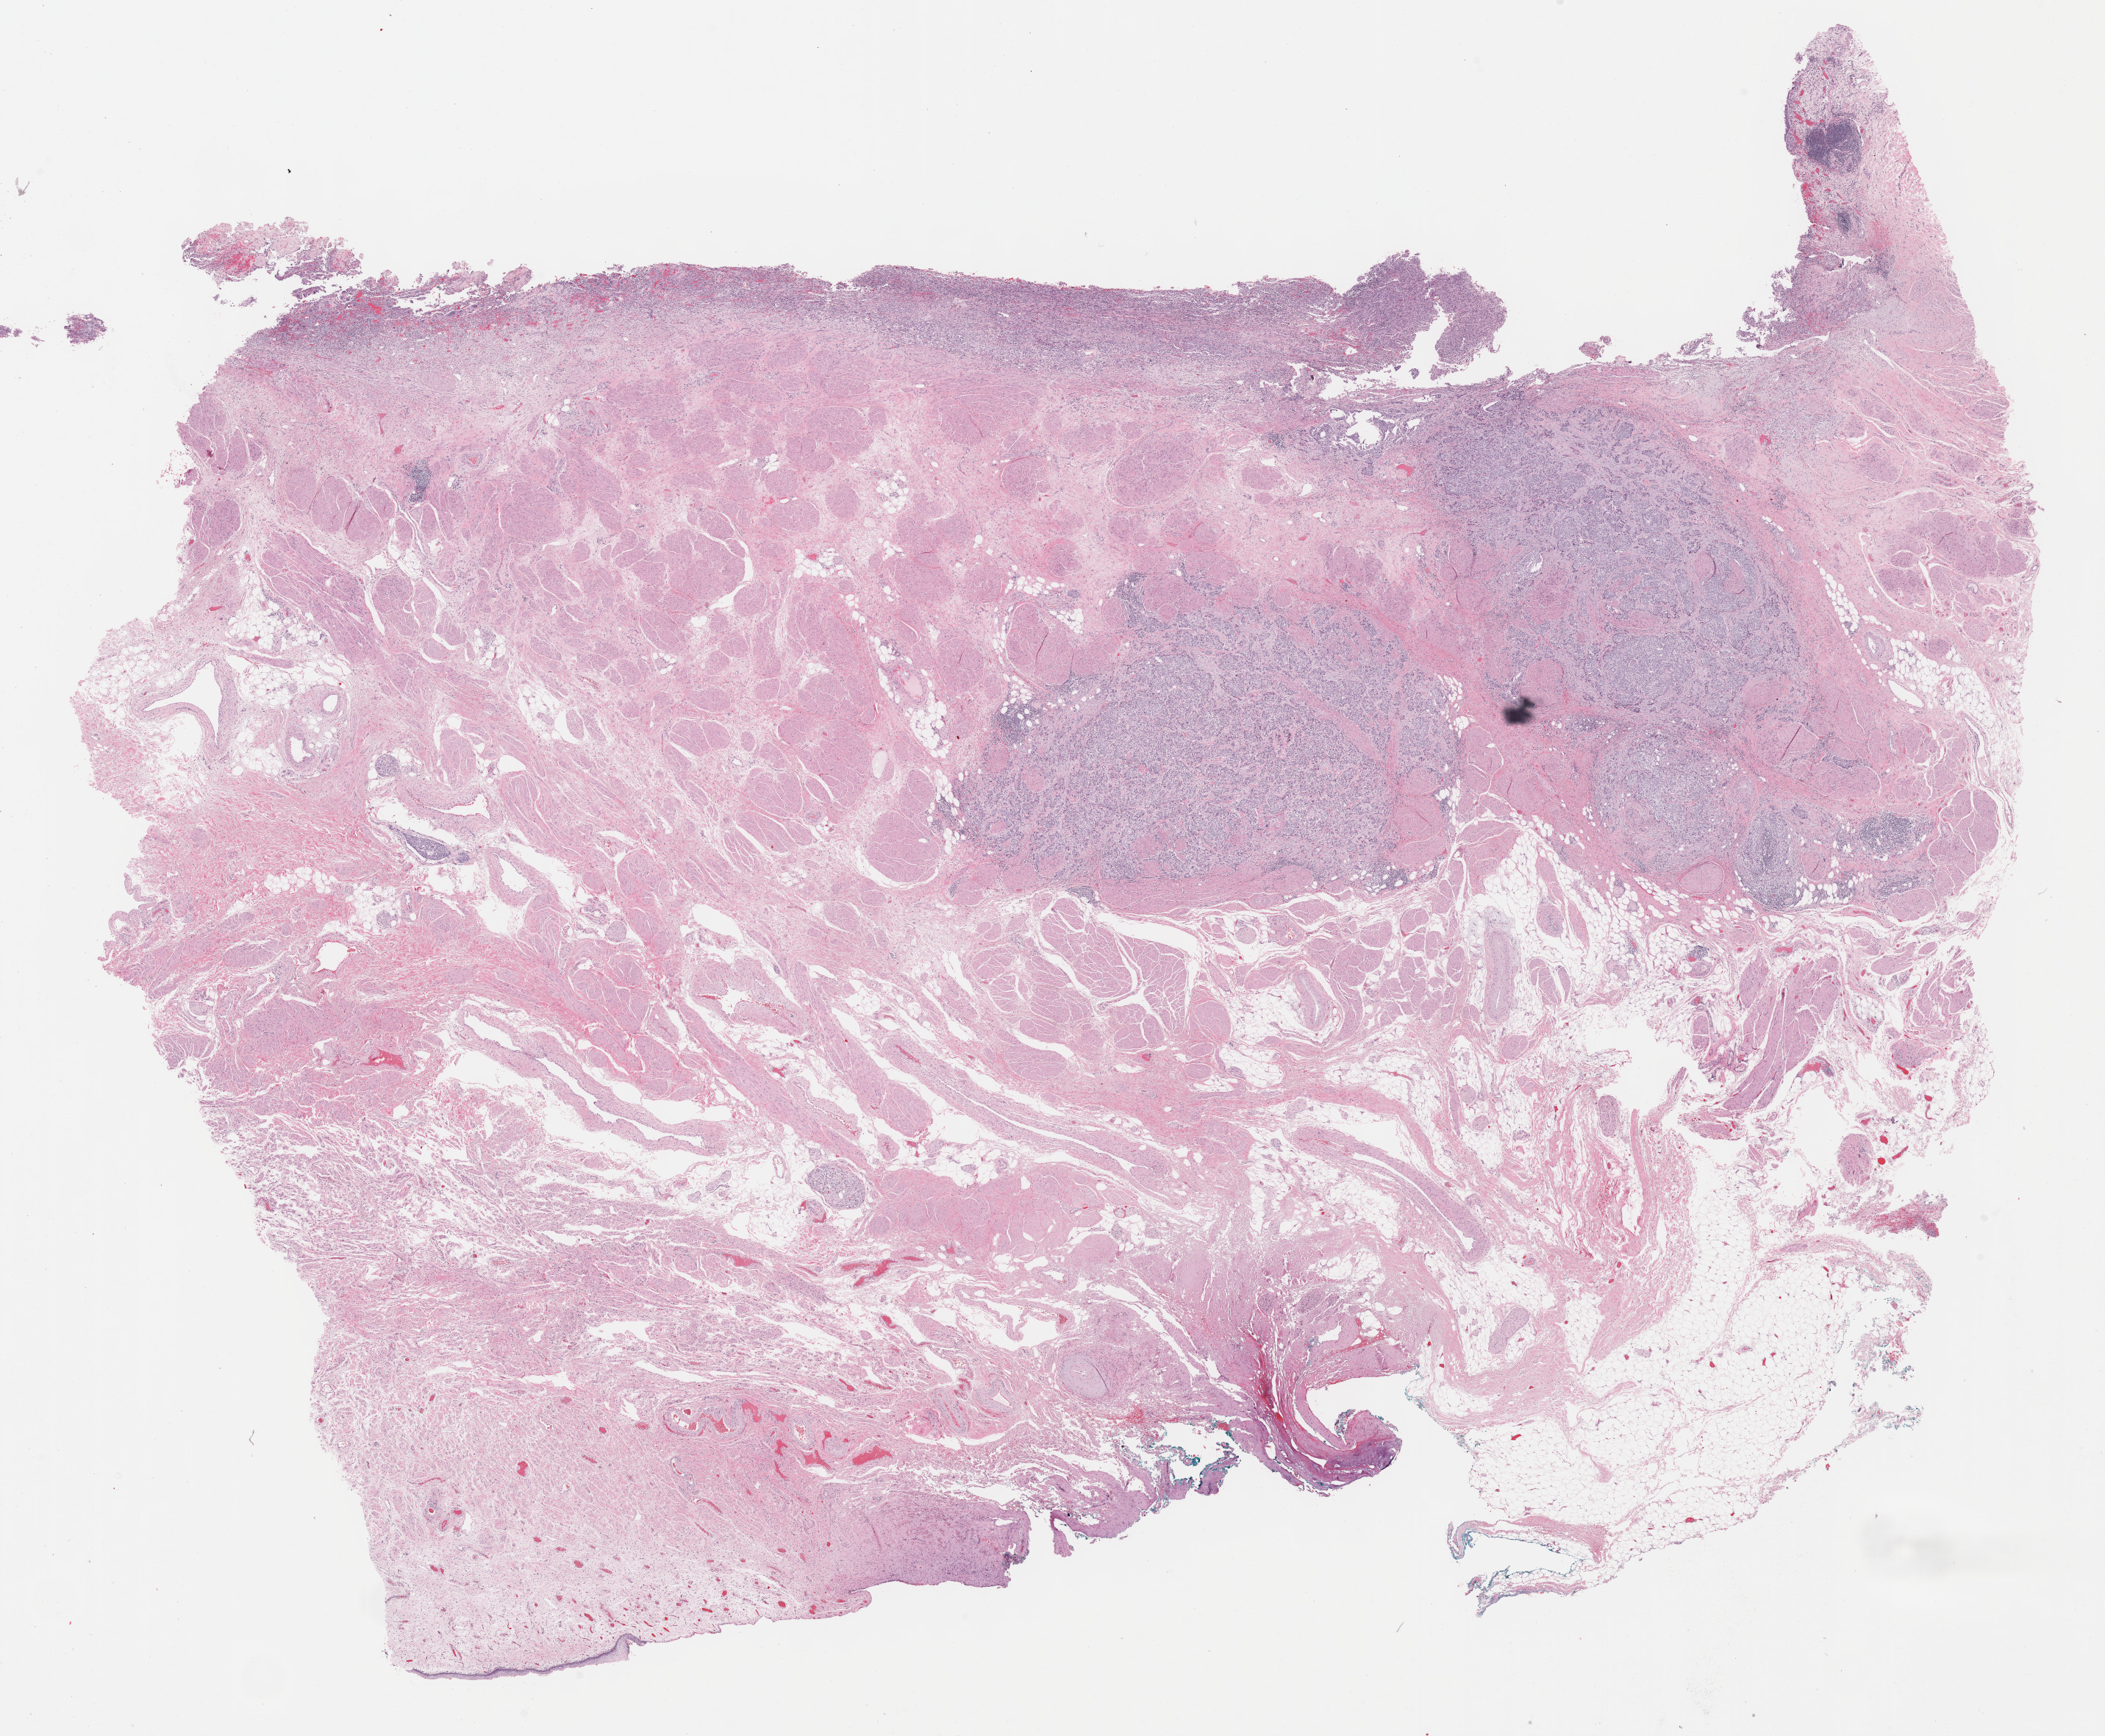
H&E whole-slide image — low-resolution overview of the scanned area, about 23.2 x 19.1 mm. Formalin-fixed paraffin-embedded (FFPE) diagnostic section. Bladder, primary tumour sample. Female patient; age at initial diagnosis 79 years.
Histologic diagnosis: Transitional cell carcinoma (lateral wall of bladder).